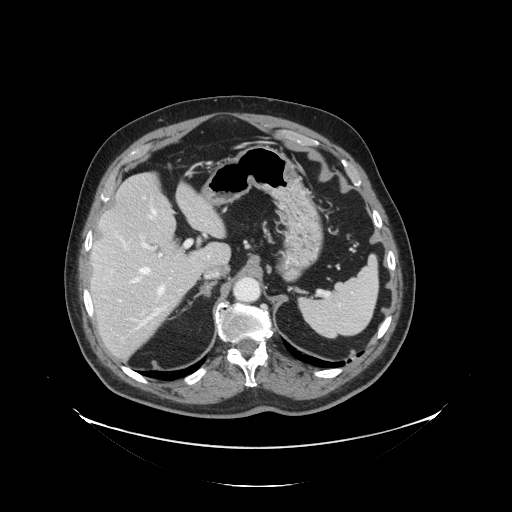
Contrast-enhanced abdominal CT, one axial slice; position 92 of 138 along the scan axis; intravenous contrast given; soft-tissue window (W 400 / L 40 HU); 512 × 512 image matrix. Male patient, age 77 years. From the clinical record (not read from this slice): diagnosis: colorectal cancer liver metastases, imaged before liver resection; multiple liver metastases: no.
Structures marked on this image (outlined manually by an expert reader):
- hepatic veins: bounding box (x1, y1, x2, y2) in pixels: (131, 209, 162, 327)
- liver: (92, 174, 230, 359)
- planned liver remnant (the part of the liver to remain after resection): (92, 174, 228, 288)
- portal vein (with intrahepatic branches): (117, 241, 191, 302)